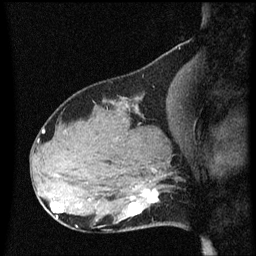
Breast MRI (dynamic contrast-enhanced), one sagittal slice. Slice 24 of 60 in the series (ordered by position). Dynamic contrast-enhanced series, image 2 of 3 at this slice position (ordered by acquisition). 1.5 T. TE 4.2 ms, TR 8.4 ms. 2 mm slice thickness. 256 × 256 image matrix, field of view 200 × 200 mm. Patient: female, 31 years. Case-level facts recorded for this patient, not image findings: setting: breast cancer imaged before/during neoadjuvant chemotherapy; receptor status: HR-positive, HER2-negative.
Outlined on this slice (semi-automatically segmented with operator editing):
- analysis volume of interest (the breast-tissue region the enhancement analysis was run in; not a lesion): bounding box (x1, y1, x2, y2) in pixels: (102, 166, 176, 229)
- tumour enhancement mask (voxels above the 70 % enhancement threshold inside the analysis volume of interest): (129, 190, 159, 215)